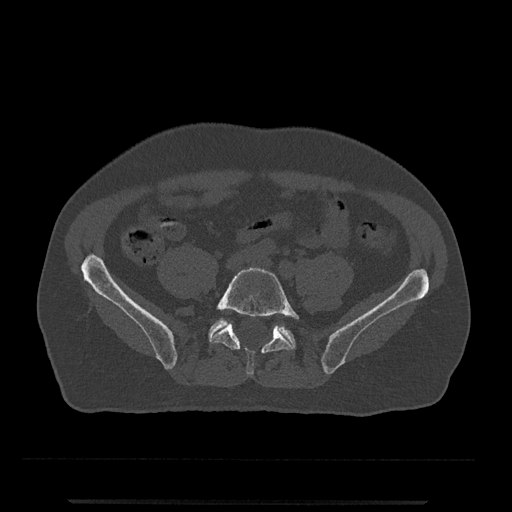
CT including the spine, one axial slice. Slice 64 of 797 in the series (ordered by position). Reconstruction kernel Br40s/3. 120 kVp. Bone window (W 1800 / L 400 HU). 0.5 mm slice thickness. 512 × 512 image matrix. Male patient, age 63 years. From the clinical record (not read from this slice): primary cancer: prostate.
Annotated regions visible in this slice (semi-automatic segmentation, software-assisted and operator-edited):
- L5 vertebra: bounding box (x1, y1, x2, y2) in pixels: (211, 267, 300, 376)